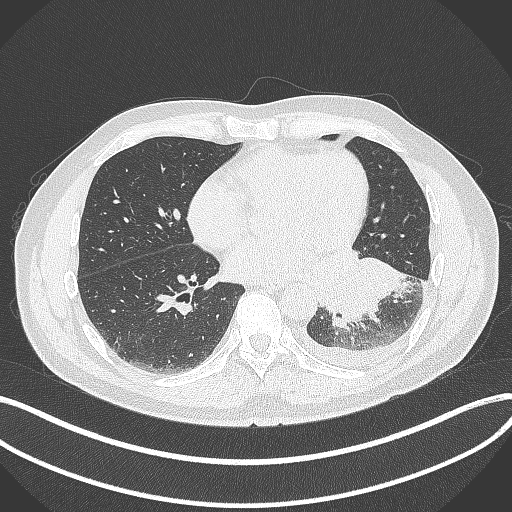
Chest CT, one axial slice. Position 145 of 342 along the scan axis. Reconstruction kernel B70f. 120 kVp. Lung window (W 1500 / L -600 HU). 1 mm slice thickness. 512 × 512 image matrix, field of view 400 × 400 mm. Patient: male, 58 years. From the clinical record (not read from this slice): clinical TNM (as recorded): T3 N1 M1b.
Outlined on this slice (bounding box drawn by a radiologist):
- lung tumour (recorded histology: small cell carcinoma): bounding box (x1, y1, x2, y2) in pixels: (301, 246, 412, 331)